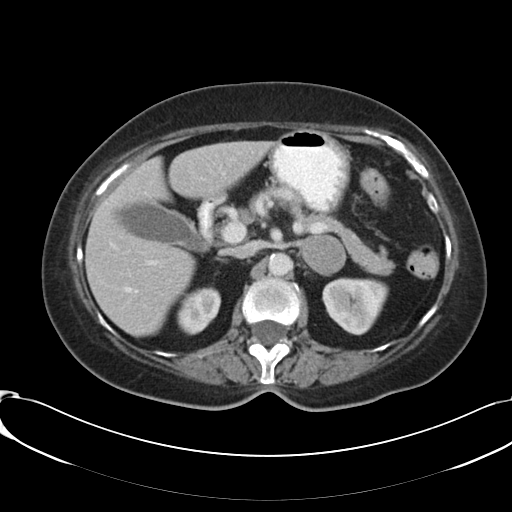
Contrast-enhanced abdominal CT, one axial slice; position 68 of 91 along the scan axis; reconstruction kernel B30f; 120 kVp; soft-tissue window (W 400 / L 40 HU); 512 × 512 image matrix. Patient: female, 73 years. From the clinical record (not read from this slice): diagnosis: adrenocortical carcinoma; tumour side: left adrenal; tumour size at pathology: 4.9 cm; Ki-67 index: 10 %; stage (as recorded): 3.
Structures marked on this image (semi-automatically segmented with operator editing):
- mass: bounding box <302,235,346,275> (left, top, right, bottom; pixels)